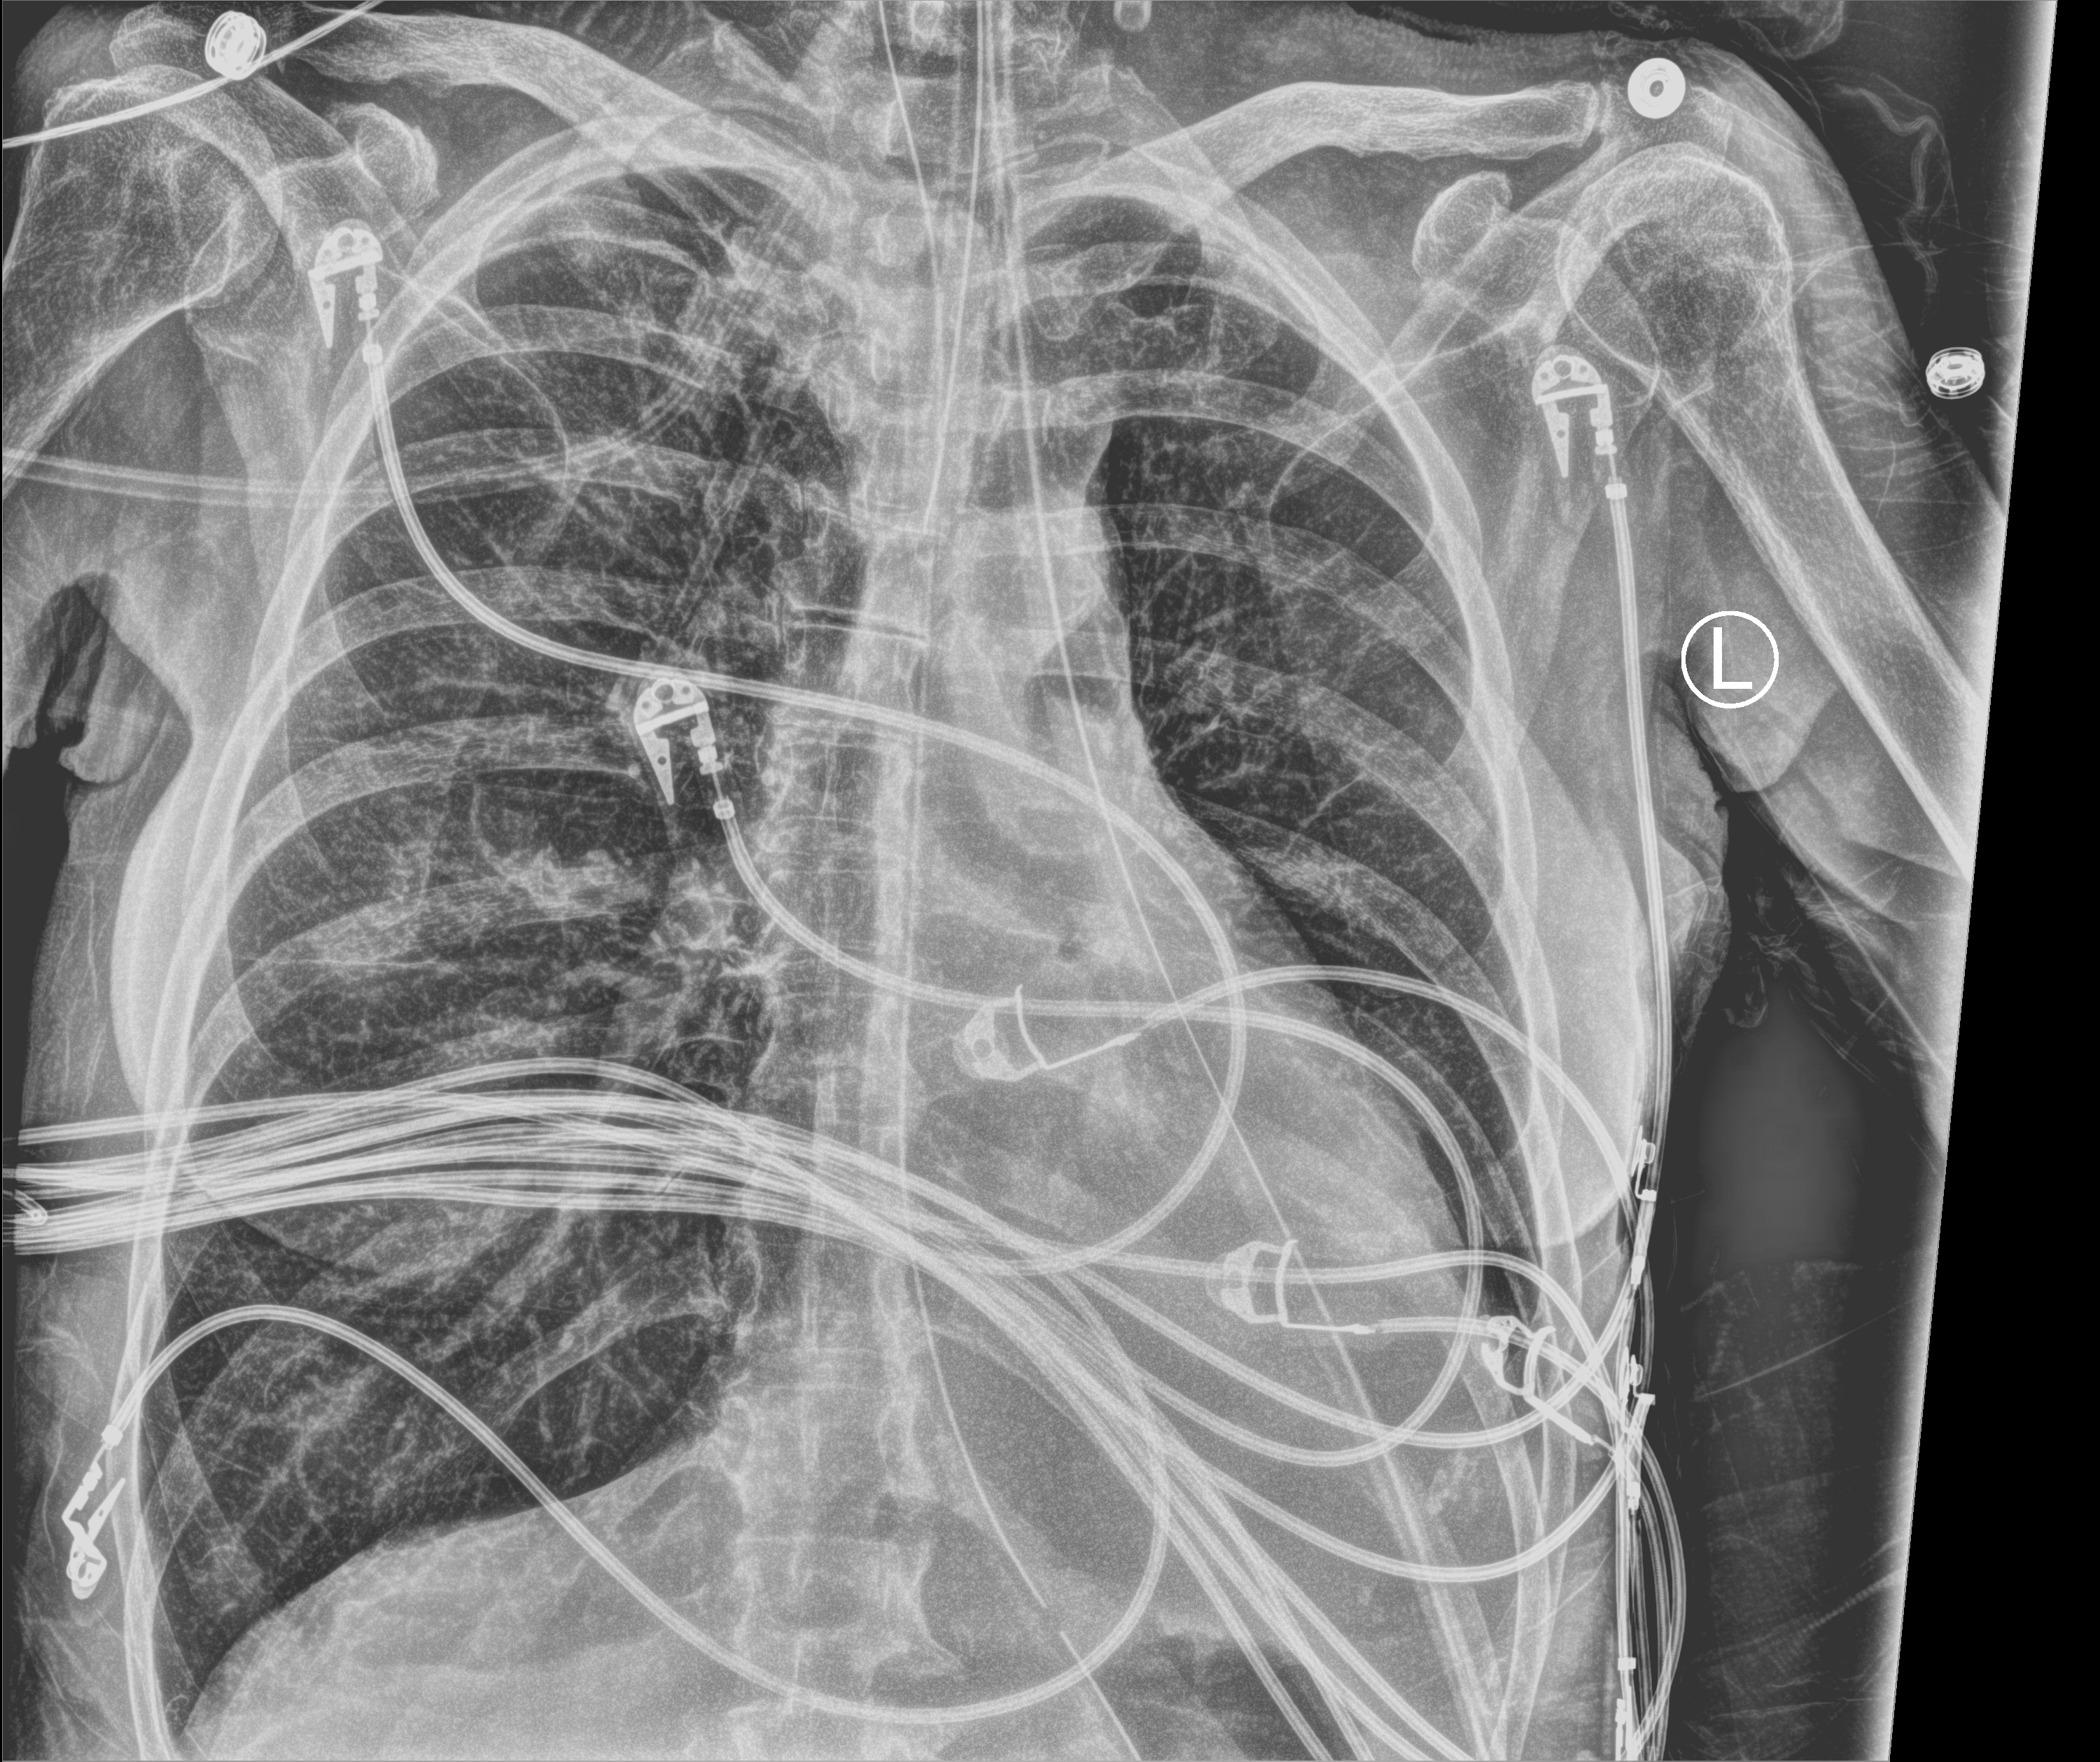
Chest X-ray (portable), anteroposterior (AP) projection. Female patient hospitalised with COVID-19, age 60–74 years.
Admission-level facts for this patient (not findings on this image; timing relative to this image not recorded): mechanically ventilated during this hospital stay: yes.